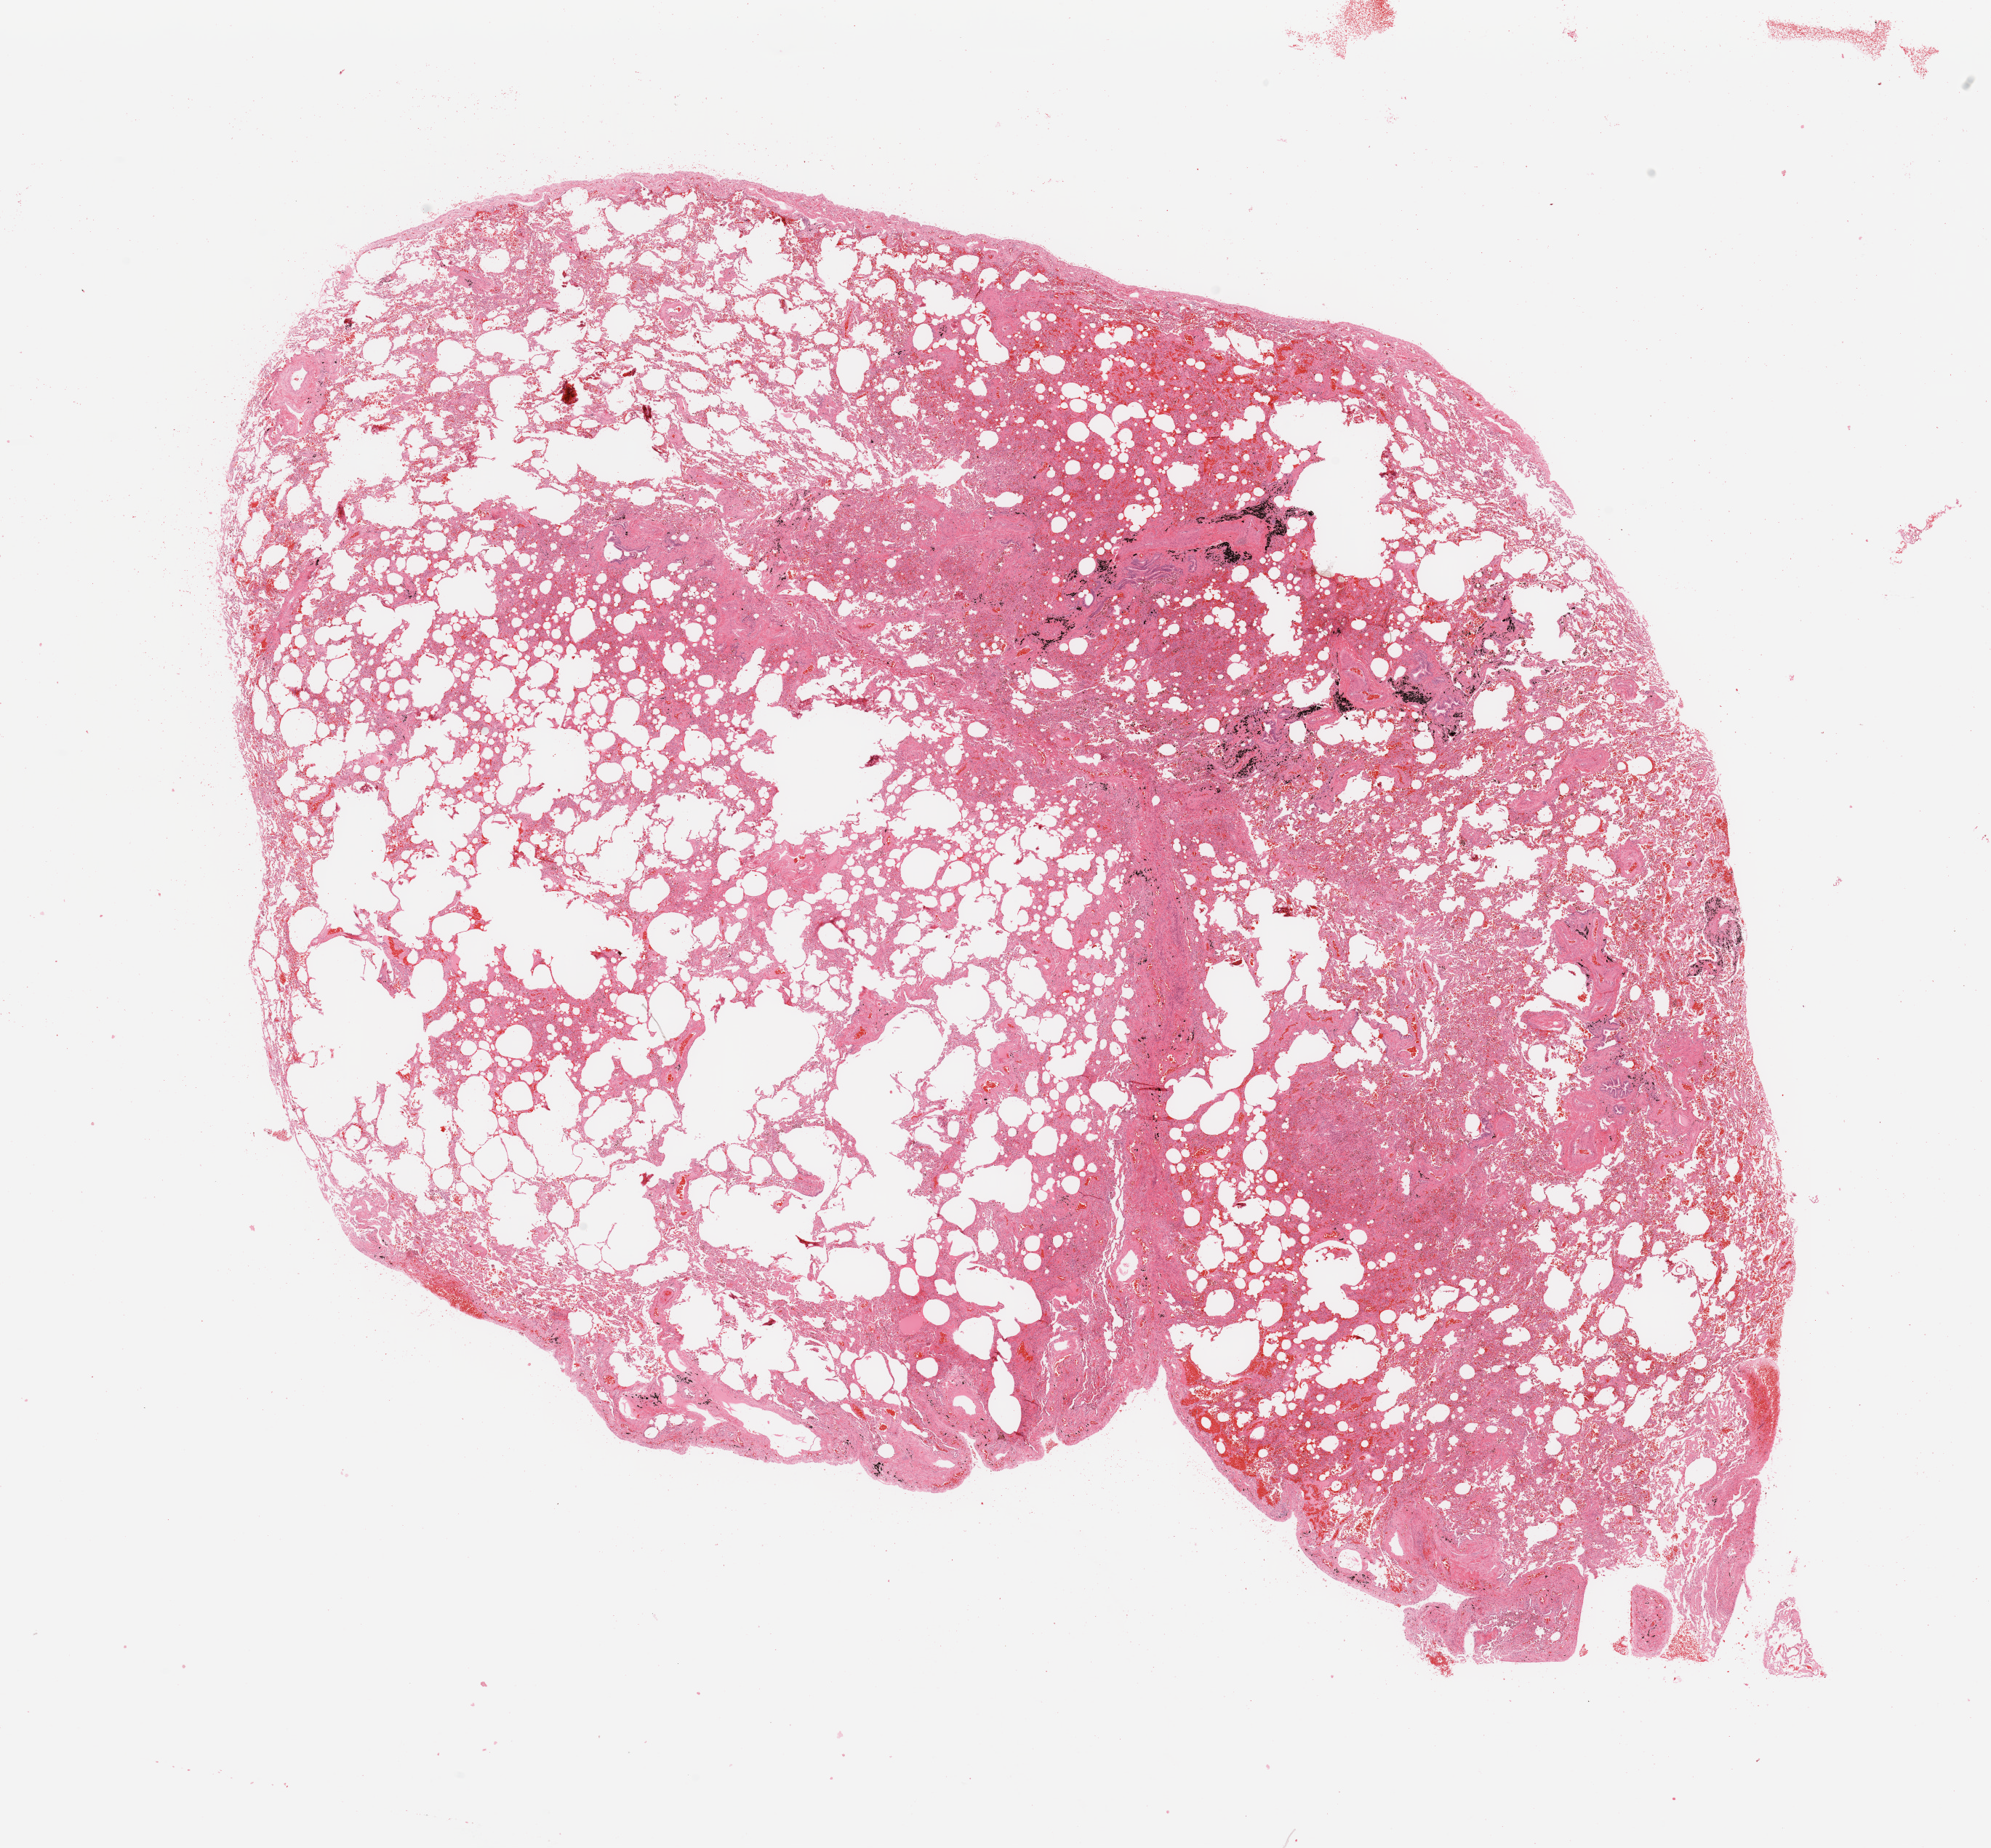
H&E-stained whole-slide image, whole scanned area (about 21.7 x 20.1 mm, slide scanned at 20x) shown as a low-resolution overview. Lung, normal (non-tumour) tissue. Male, 71 y/o.
This section: normal (non-tumour) tissue from the same patient. Patient diagnosis: Adenocarcinoma, NOS.